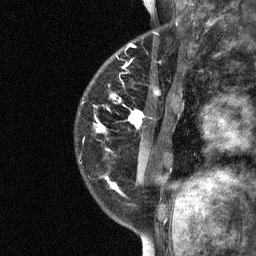
Breast MRI (dynamic contrast-enhanced), one sagittal slice; position 19 of 64 along the scan axis; dynamic contrast-enhanced study with each time point stored as its own series, time point 2 of 3 at this slice position (early post-contrast, ordered by acquisition time); 1.5 T; TE 4.8 ms, TR 27 ms; 2 mm slice thickness; 256 × 256 image matrix, field of view 180 × 180 mm. Female patient, age 34 years. Case-level facts recorded for this patient, not image findings: setting: breast cancer imaged before/during neoadjuvant chemotherapy; receptor status: HR-positive, HER2-negative.
Annotated regions visible in this slice (semi-automatically segmented with operator editing):
- analysis volume of interest (the breast-tissue region the enhancement analysis was run in; not a lesion): bounding box (x1, y1, x2, y2) in pixels: (78, 44, 181, 191)
- tumour enhancement mask (voxels above the 90 % enhancement threshold inside the analysis volume of interest): (97, 99, 143, 189)